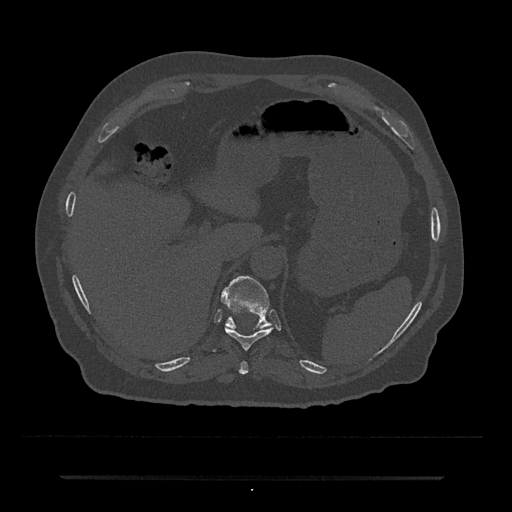
CT including the spine, one axial slice. Position 214 of 797 along the scan axis. Bone window (W 1800 / L 400 HU). 512 × 512 image matrix, field of view 437 × 437 mm. Male patient, age 69 years. Case-level facts recorded for this patient, not image findings: primary cancer: prostate.
Structures marked on this image (semi-automatically segmented with operator editing):
- T10 vertebra: box from (x=213, y=326) to (x=273, y=351) px
- T11 vertebra: (x=220, y=276)–(x=272, y=329)
- T9 vertebra: (x=239, y=361)–(x=249, y=374)